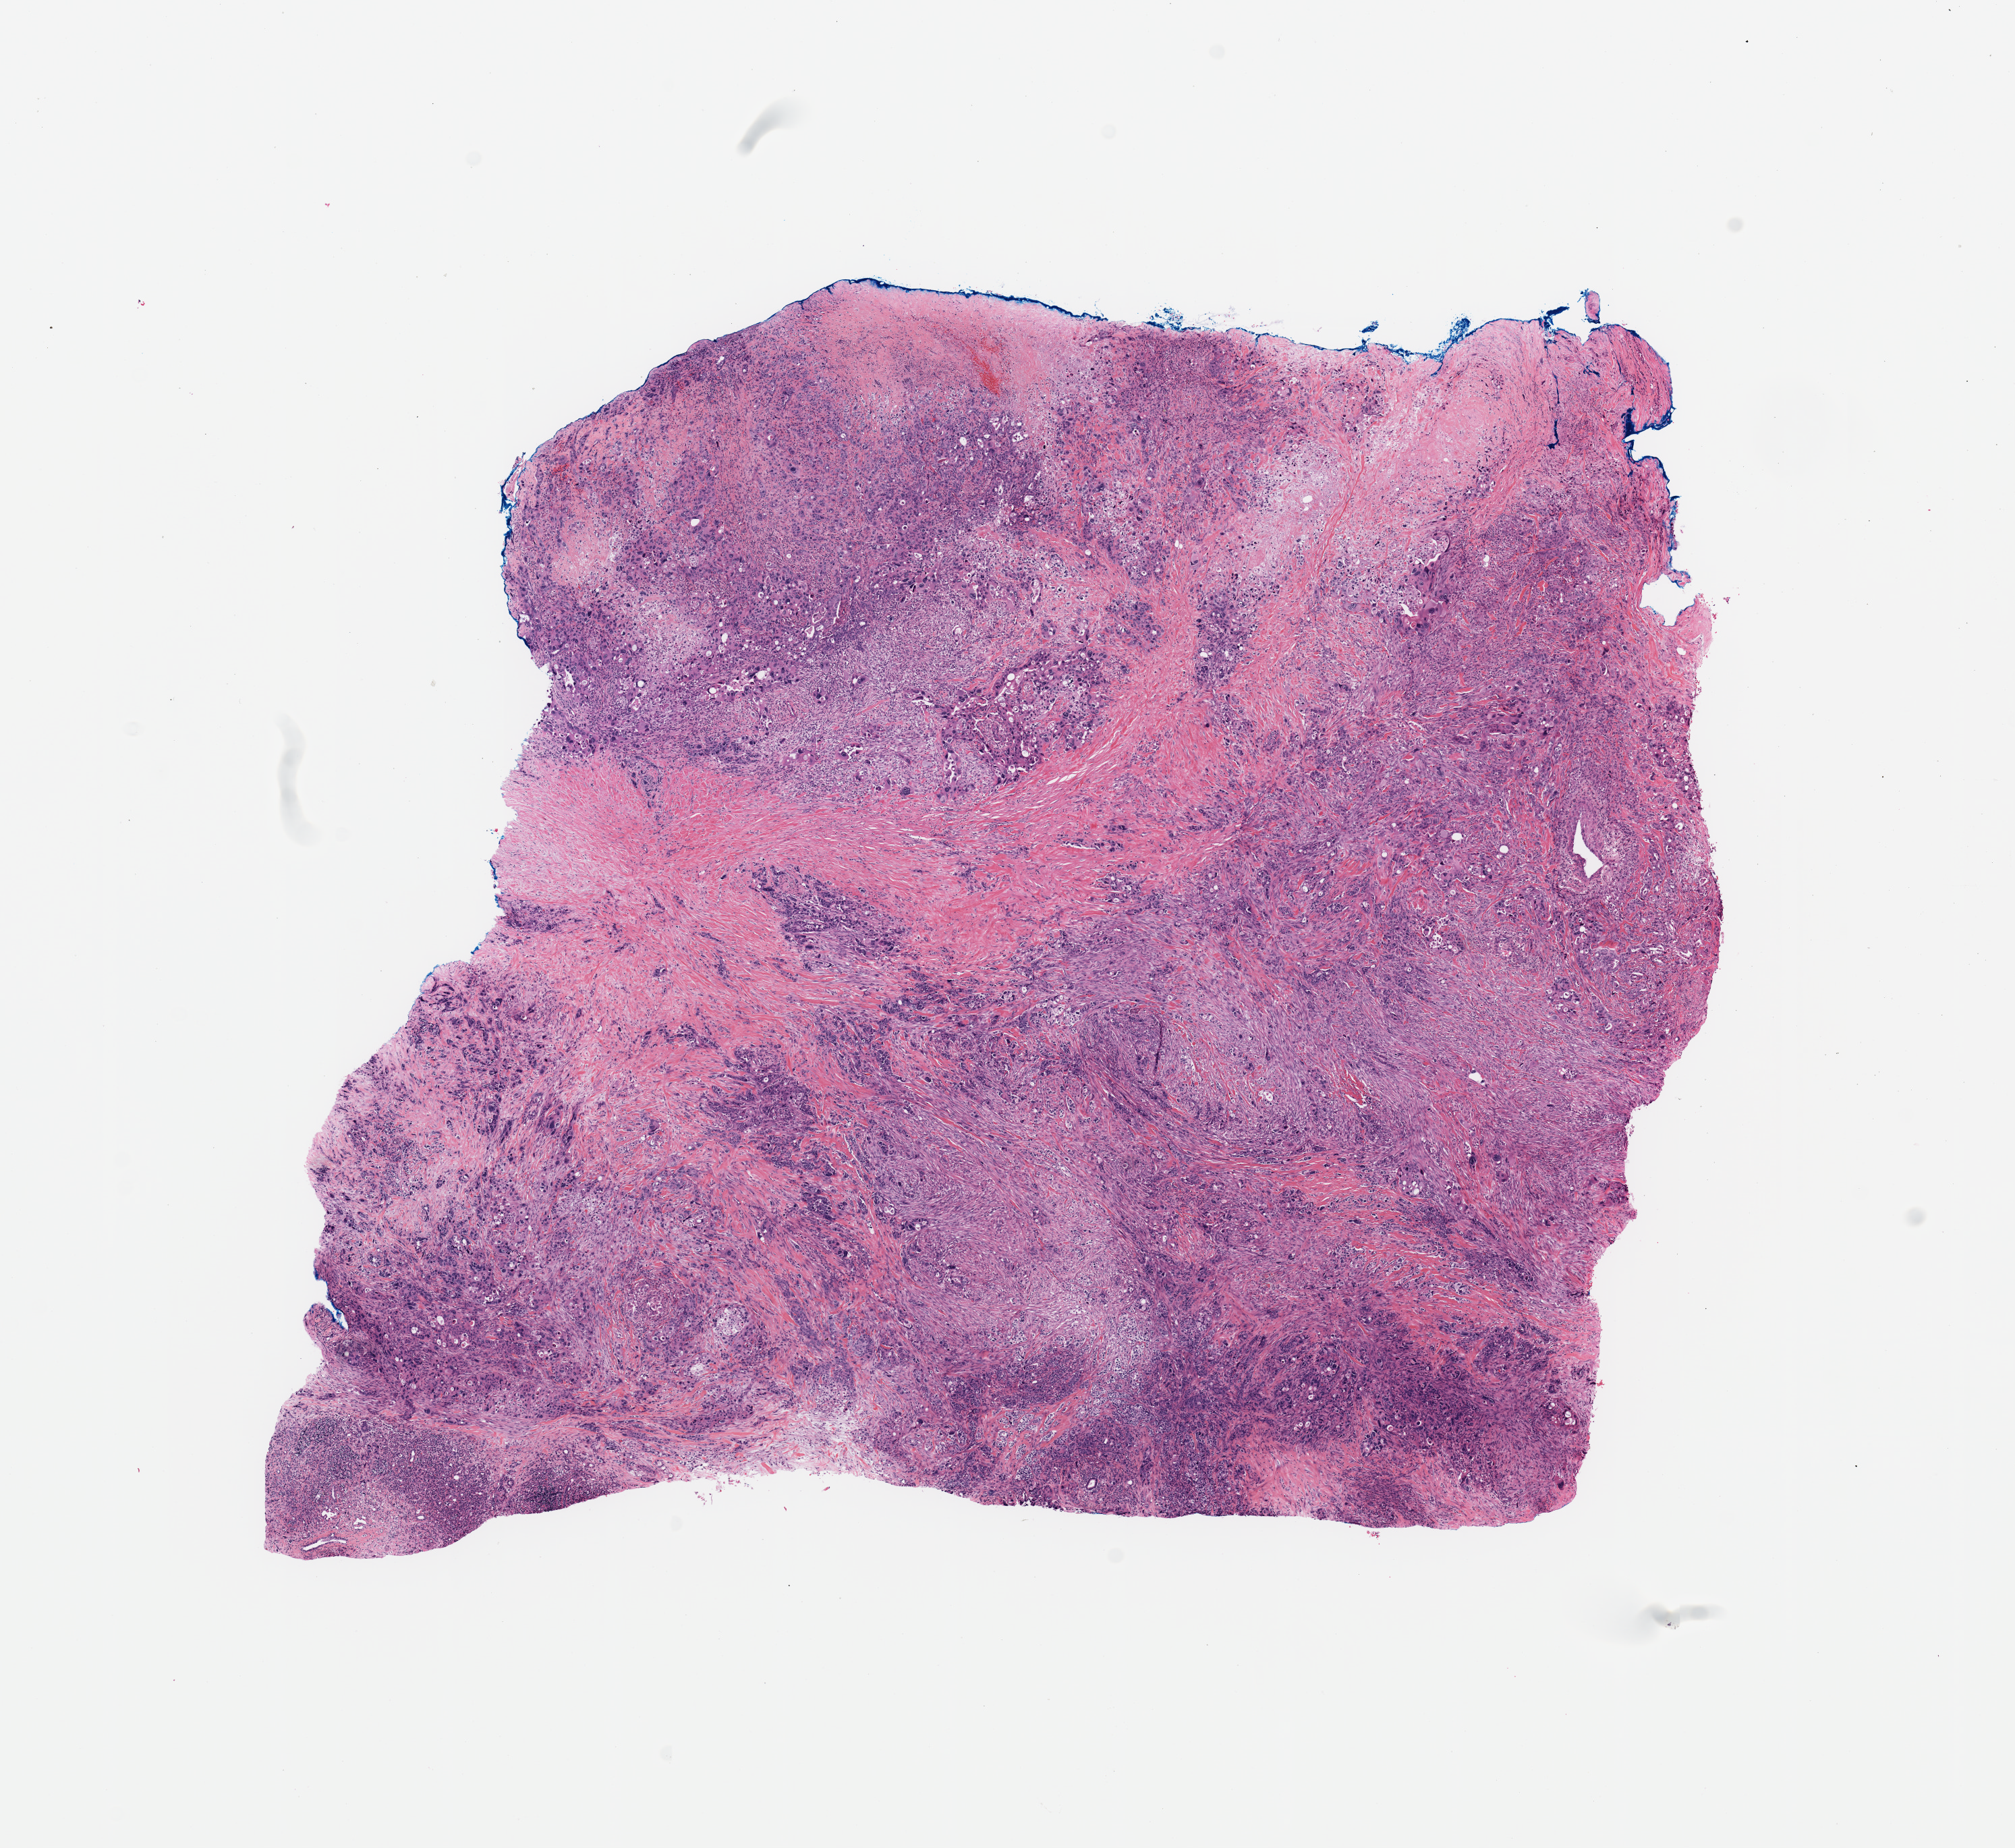
Digitized Hematoxylin and eosin (H&E) stained tissue section (whole slide) — whole scanned area (about 11.8 x 10.8 mm, from a 20x scan) shown as a low-resolution overview; tumour tissue sample, pancreas. 52-year-old female patient. Histologic grade: G3 (poorly differentiated).
AJCC pathologic stage: IIB. Primary tumour site (as recorded): head. Diagnosis: Infiltrating duct carcinoma, NOS.